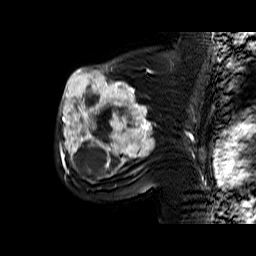
Breast MRI (dynamic contrast-enhanced), one sagittal slice. Slice 40 of 60 in the series (ordered by position). Dynamic contrast-enhanced series, time point 2 of 6 at this slice position (early post-contrast). 1.5 T. TE 6.4 ms, TR 32.9 ms. 4 mm slice thickness. 256 × 256 image matrix. Female patient. Case-level facts recorded for this patient, not image findings: setting: breast cancer imaged before/during neoadjuvant chemotherapy; receptor status: triple-negative.
Outlined on this slice (semi-automatic segmentation, software-assisted and operator-edited):
- analysis volume of interest (the breast-tissue region the enhancement analysis was run in; not a lesion): bounding box <56,65,156,174> (left, top, right, bottom; pixels)
- tumour enhancement mask (voxels above the 100 % enhancement threshold inside the analysis volume of interest): <60,65,156,174>